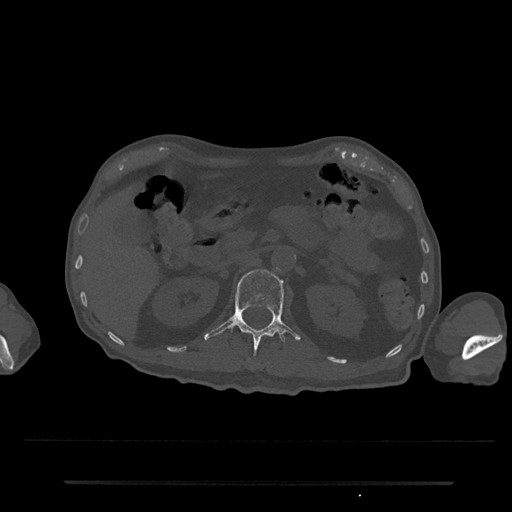
CT including the spine, one axial slice; position 130 of 797 along the scan axis; bone window (W 1800 / L 400 HU); 512 × 512 image matrix, field of view 427 × 427 mm. Male patient, age 74 years. From the clinical record (not read from this slice): primary cancer: prostate.
Structures marked on this image (semi-automatic segmentation, software-assisted and operator-edited):
- L1 vertebra: box from (x=204, y=269) to (x=301, y=350) px